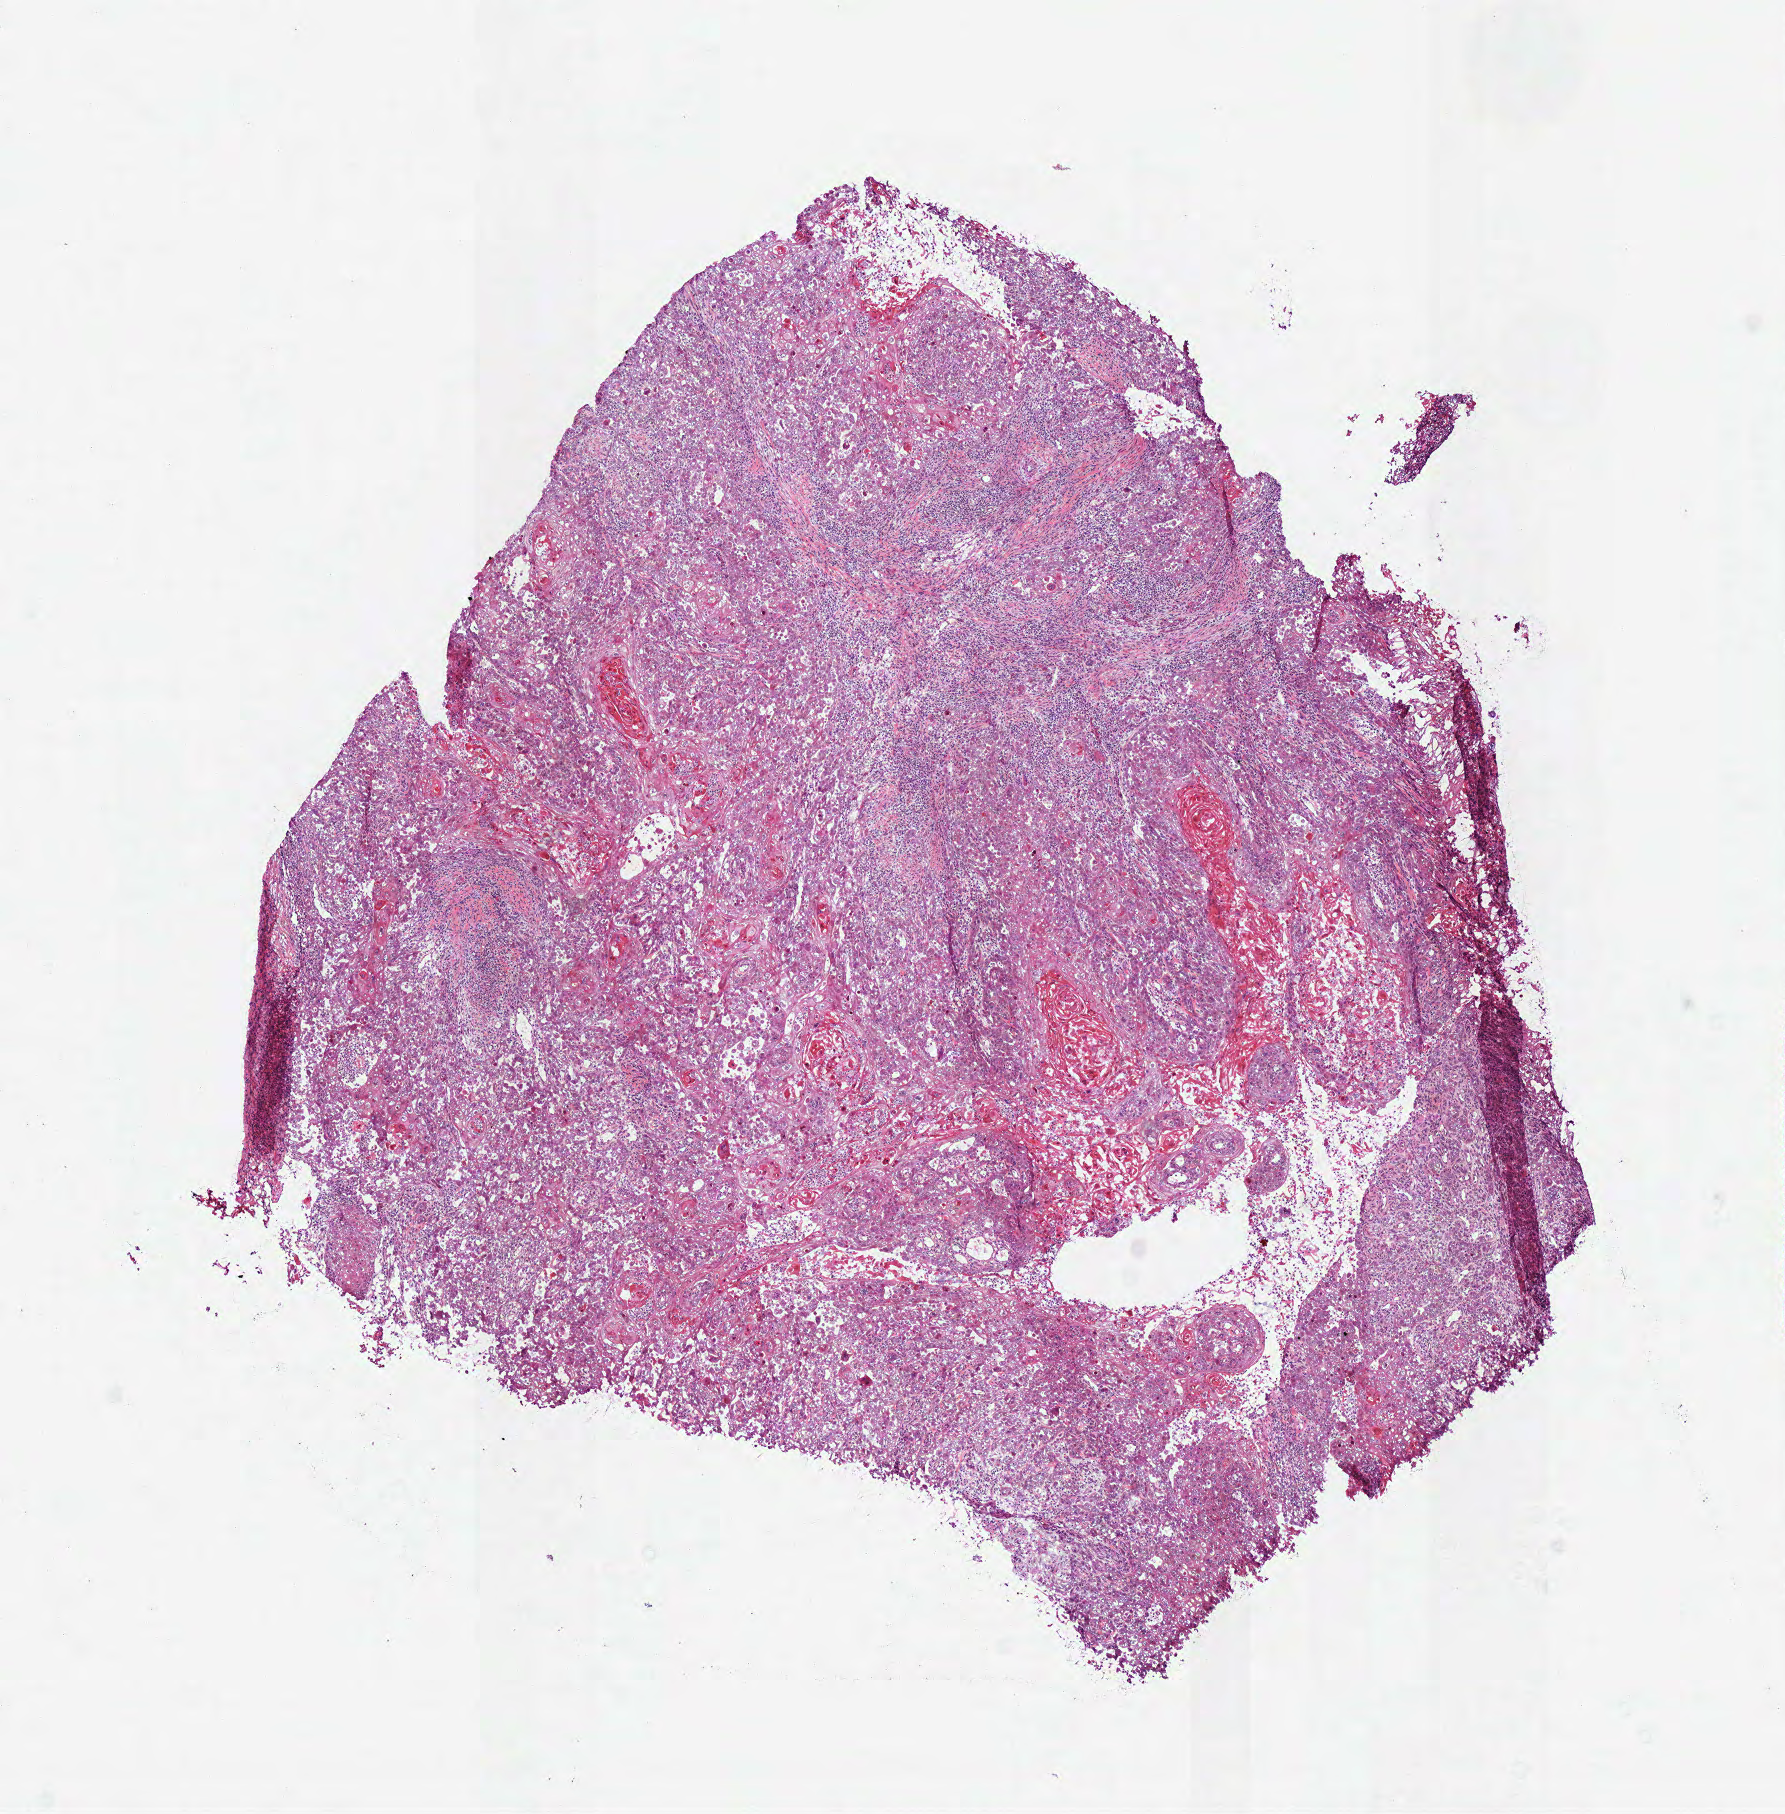
Digitized Hematoxylin and eosin (H&E) stained tissue section (whole slide) — a low-resolution overview of the entire scanned area, about 7.0 x 7.1 mm. Frozen section from the bottom of the tissue portion. Sample: primary tumour, head and neck. Male, age 61 years at initial diagnosis. Pathologist review of this section (percent, as recorded): tumour cells 90%, tumour nuclei 60%.
Pathologic diagnosis: Squamous cell carcinoma, NOS (larynx, NOS).